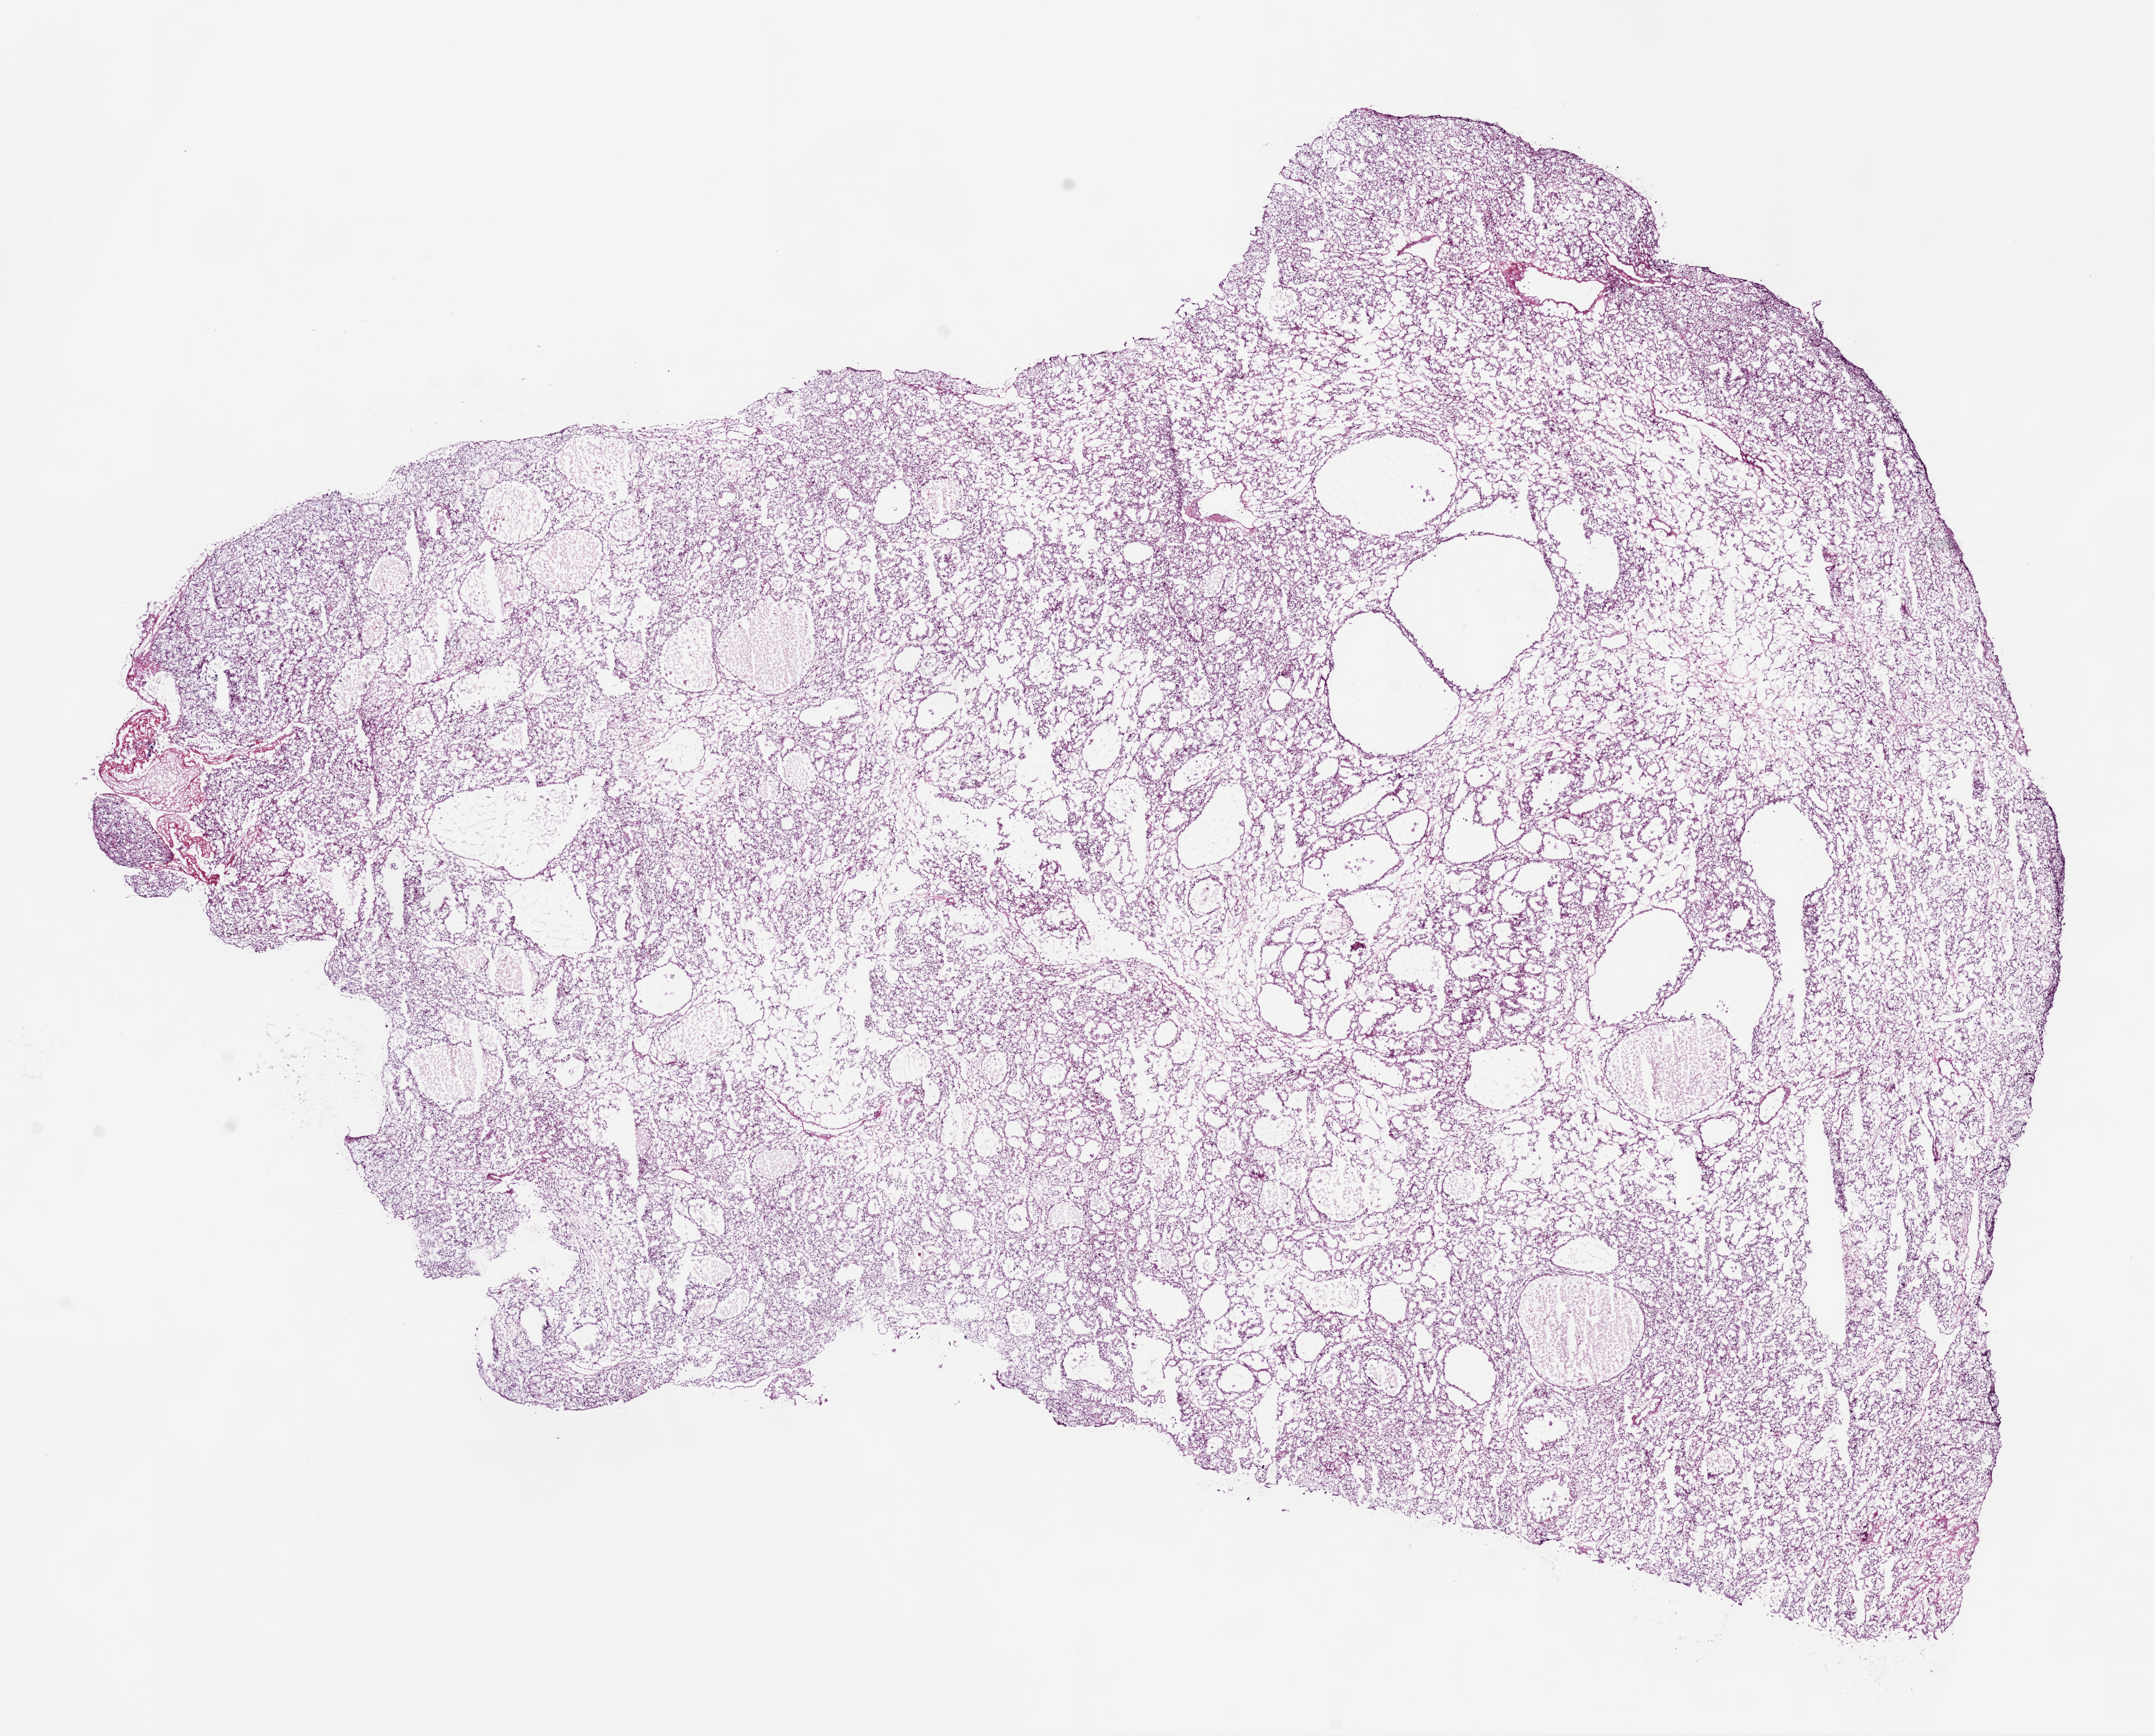
Whole-slide histology image, Hematoxylin and eosin (H&E) stained, whole scanned area (about 14.0 x 11.3 mm, from a 20x scan) shown as a low-resolution overview; frozen section from the bottom of the tissue portion; kidney, primary tumour sample. Patient: male, age at initial diagnosis 75 years. Histologic grade: G2 (moderately differentiated). Slide review estimates, as recorded: tumour cells 95%, tumour nuclei 90%, normal cells 0%, stromal cells 5%, necrosis 0%.
AJCC pathologic stage: III. Pathologic diagnosis: Clear cell adenocarcinoma, NOS. Laterality: right. TNM: T3a NX M0.